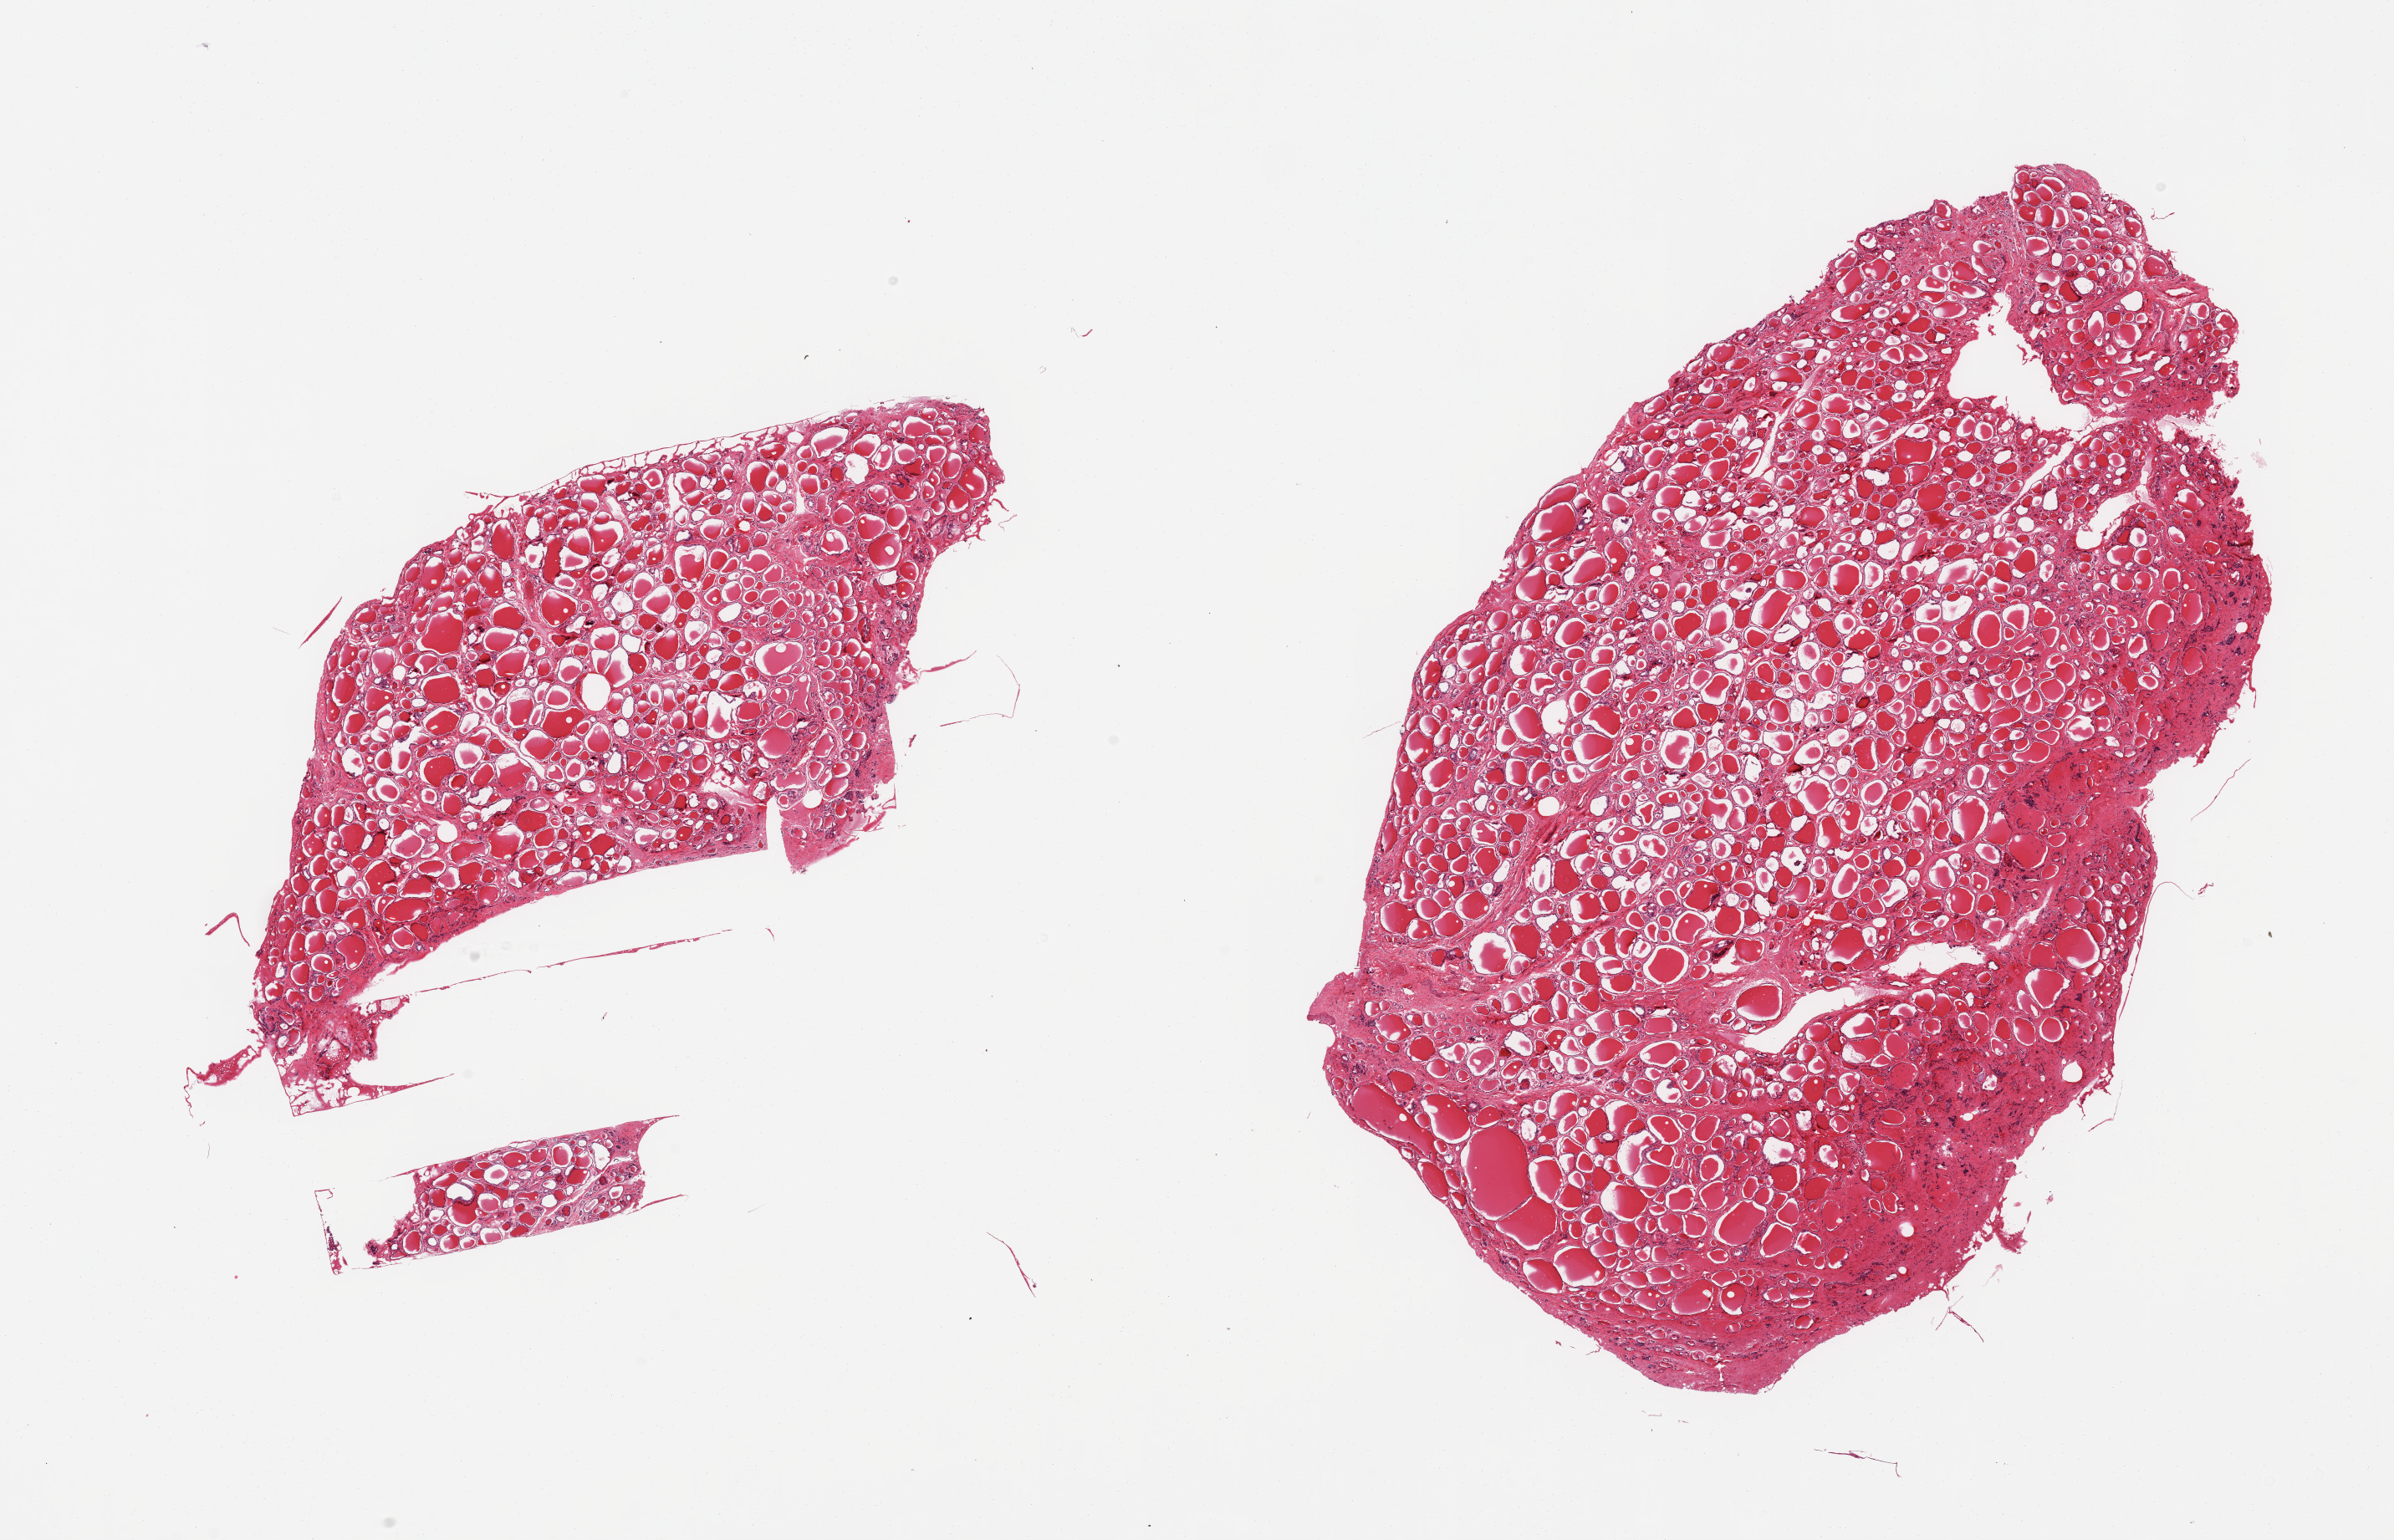
Haematoxylin and eosin whole-slide image, brightfield, whole scanned area (about 22.6 x 14.6 mm, acquisition: 20x scan) shown as a low-resolution overview, PAXgene-fixed, paraffin-embedded tissue, target tissue: thyroid, donor tissue sample. Donor sex: male.
Pathologist's review note for this sample: 2 pieces, no abnormalities.